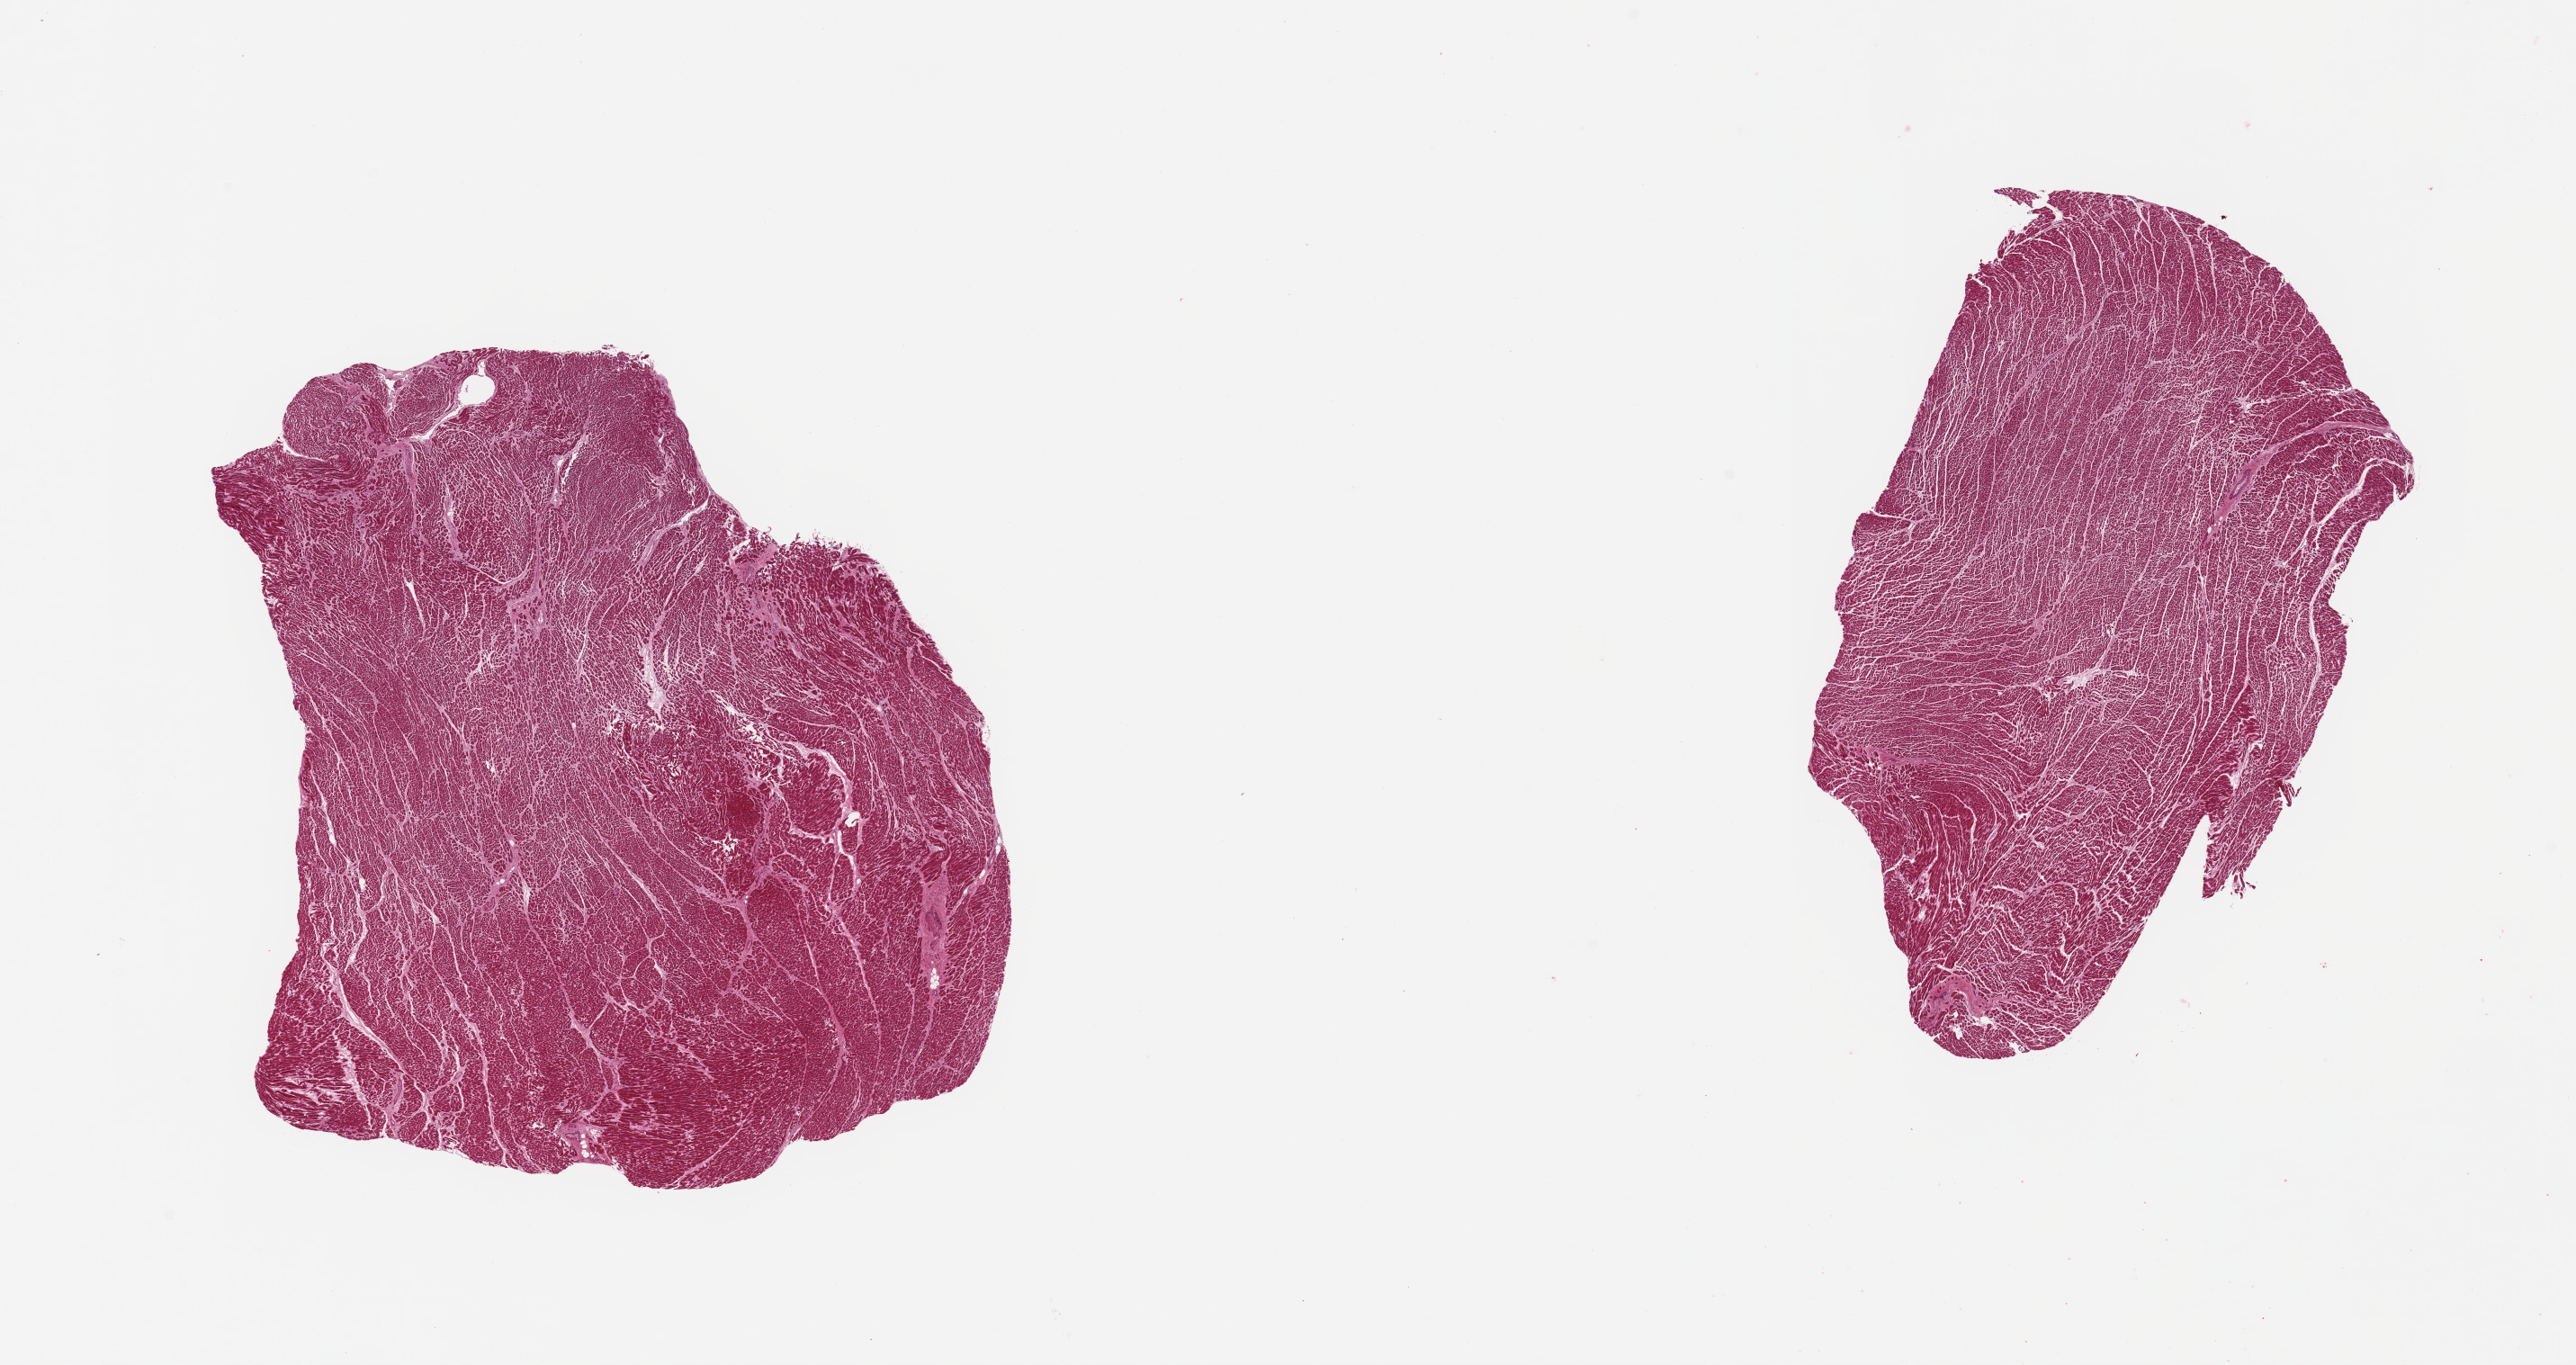
Digitized H&E-stained section — shown as a low-resolution overview of the whole scanned area (about 22.6 x 12.0 mm); PAXgene-fixed paraffin-embedded (PFPE) section; sampled site (target tissue): heart; tissue donor sample. Male donor.
Pathologist's review note for this sample: 2 pieces; no lesions.